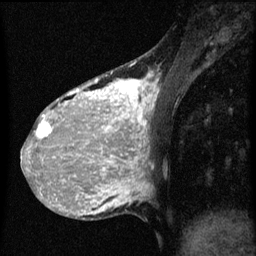
Breast MRI (dynamic contrast-enhanced), one sagittal slice; dynamic contrast-enhanced series, image 2 of 3 at this slice position (ordered by acquisition); 1.5 T; TE 4.2 ms, TR 8 ms; 256 × 256 image matrix, field of view 180 × 180 mm. Patient: female, 36 years.
Annotated regions visible in this slice (semi-automatically segmented with operator editing):
- analysis volume of interest (the breast-tissue region the enhancement analysis was run in; not a lesion): bounding box (x1, y1, x2, y2) in pixels: (32, 68, 161, 161)
- tumour enhancement mask (voxels above the 70 % enhancement threshold inside the analysis volume of interest): (34, 76, 159, 161)